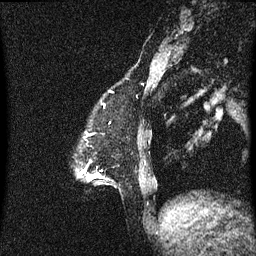
Breast MRI (dynamic contrast-enhanced), one sagittal slice; position 11 of 60 along the scan axis; dynamic contrast-enhanced series, image 2 of 3 at this slice position (ordered by acquisition); 1.5 T; TE 4.2 ms, TR 8.4 ms; 2 mm slice thickness; 256 × 256 image matrix, field of view 200 × 200 mm. Patient: female, 47 years.
Annotated regions visible in this slice (semi-automatic segmentation, software-assisted and operator-edited):
- analysis volume of interest (the breast-tissue region the enhancement analysis was run in; not a lesion): bounding box [x1, y1, x2, y2] px = [81, 170, 103, 181]
- tumour enhancement mask (voxels above the 70 % enhancement threshold inside the analysis volume of interest): [81, 170, 91, 179]